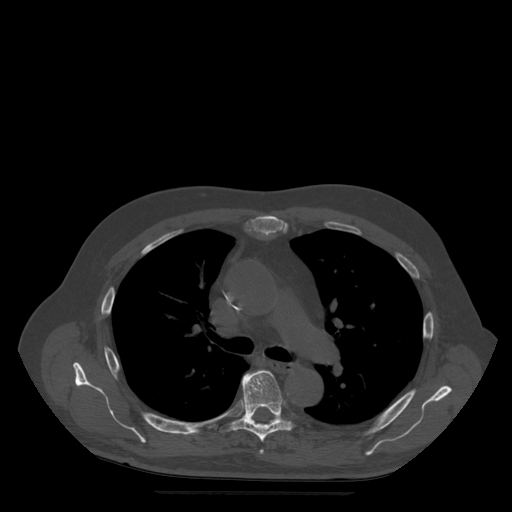
CT including the spine, one axial slice; position 355 of 522 along the scan axis; bone window (W 1800 / L 400 HU); 512 × 512 image matrix, field of view 420 × 420 mm. Patient age 72 years. From the clinical record (not read from this slice): primary cancer: prostate.
Annotated regions visible in this slice (semi-automatically segmented with operator editing):
- T5 vertebra: bounding box (x1, y1, x2, y2) in pixels: (260, 450, 264, 454)
- T6 vertebra: (220, 370, 295, 442)
- T7 vertebra: (254, 420, 276, 422)